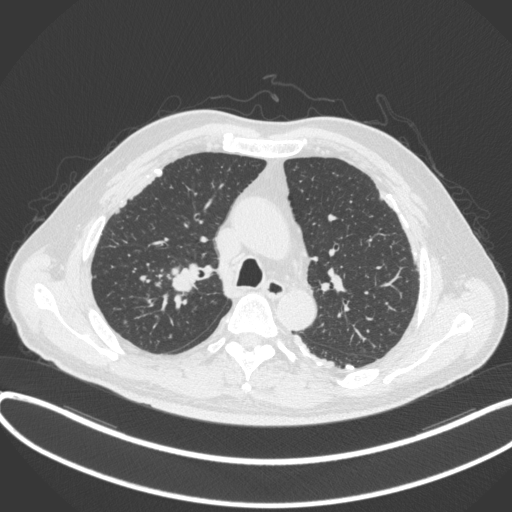
Chest CT, one axial slice. Position 293 of 455 along the scan axis. Reconstruction kernel B31f. 120 kVp. Lung window (W 1500 / L -600 HU). 512 × 512 image matrix, field of view 400 × 400 mm. Patient: male, 58 years. From the clinical record (not read from this slice): clinical TNM (as recorded): T1c N0 M0.
Outlined on this slice (bounding box drawn by a radiologist):
- lung tumour (recorded histology: squamous cell carcinoma): bounding box (x1, y1, x2, y2) in pixels: (163, 264, 205, 298)